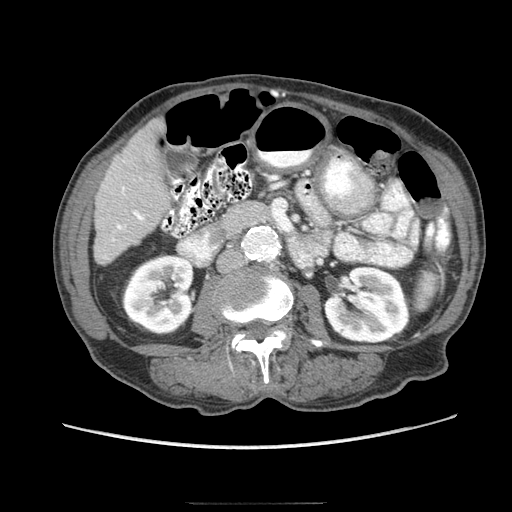
Contrast-enhanced abdominal CT (liver protocol), one axial slice; position 24 of 83 along the scan axis; soft-tissue window (W 400 / L 40 HU); 2.5 mm slice thickness; 512 × 512 image matrix, field of view 360 × 360 mm. From the clinical record (not read from this slice): diagnosis: hepatocellular carcinoma (patient treated with transarterial chemoembolisation; whether this scan precedes or follows treatment is not stated here); TNM stage (as recorded): Stage-I; Child-Pugh class: A.
Structures marked on this image (semi-automatic segmentation, software-assisted and operator-edited):
- liver parenchyma outside the tumour (the mass and vessels are separate outlines, so this box may not span the whole liver): bounding box (x1, y1, x2, y2) in pixels: (94, 120, 168, 264)
- liver vessels: (113, 187, 144, 241)